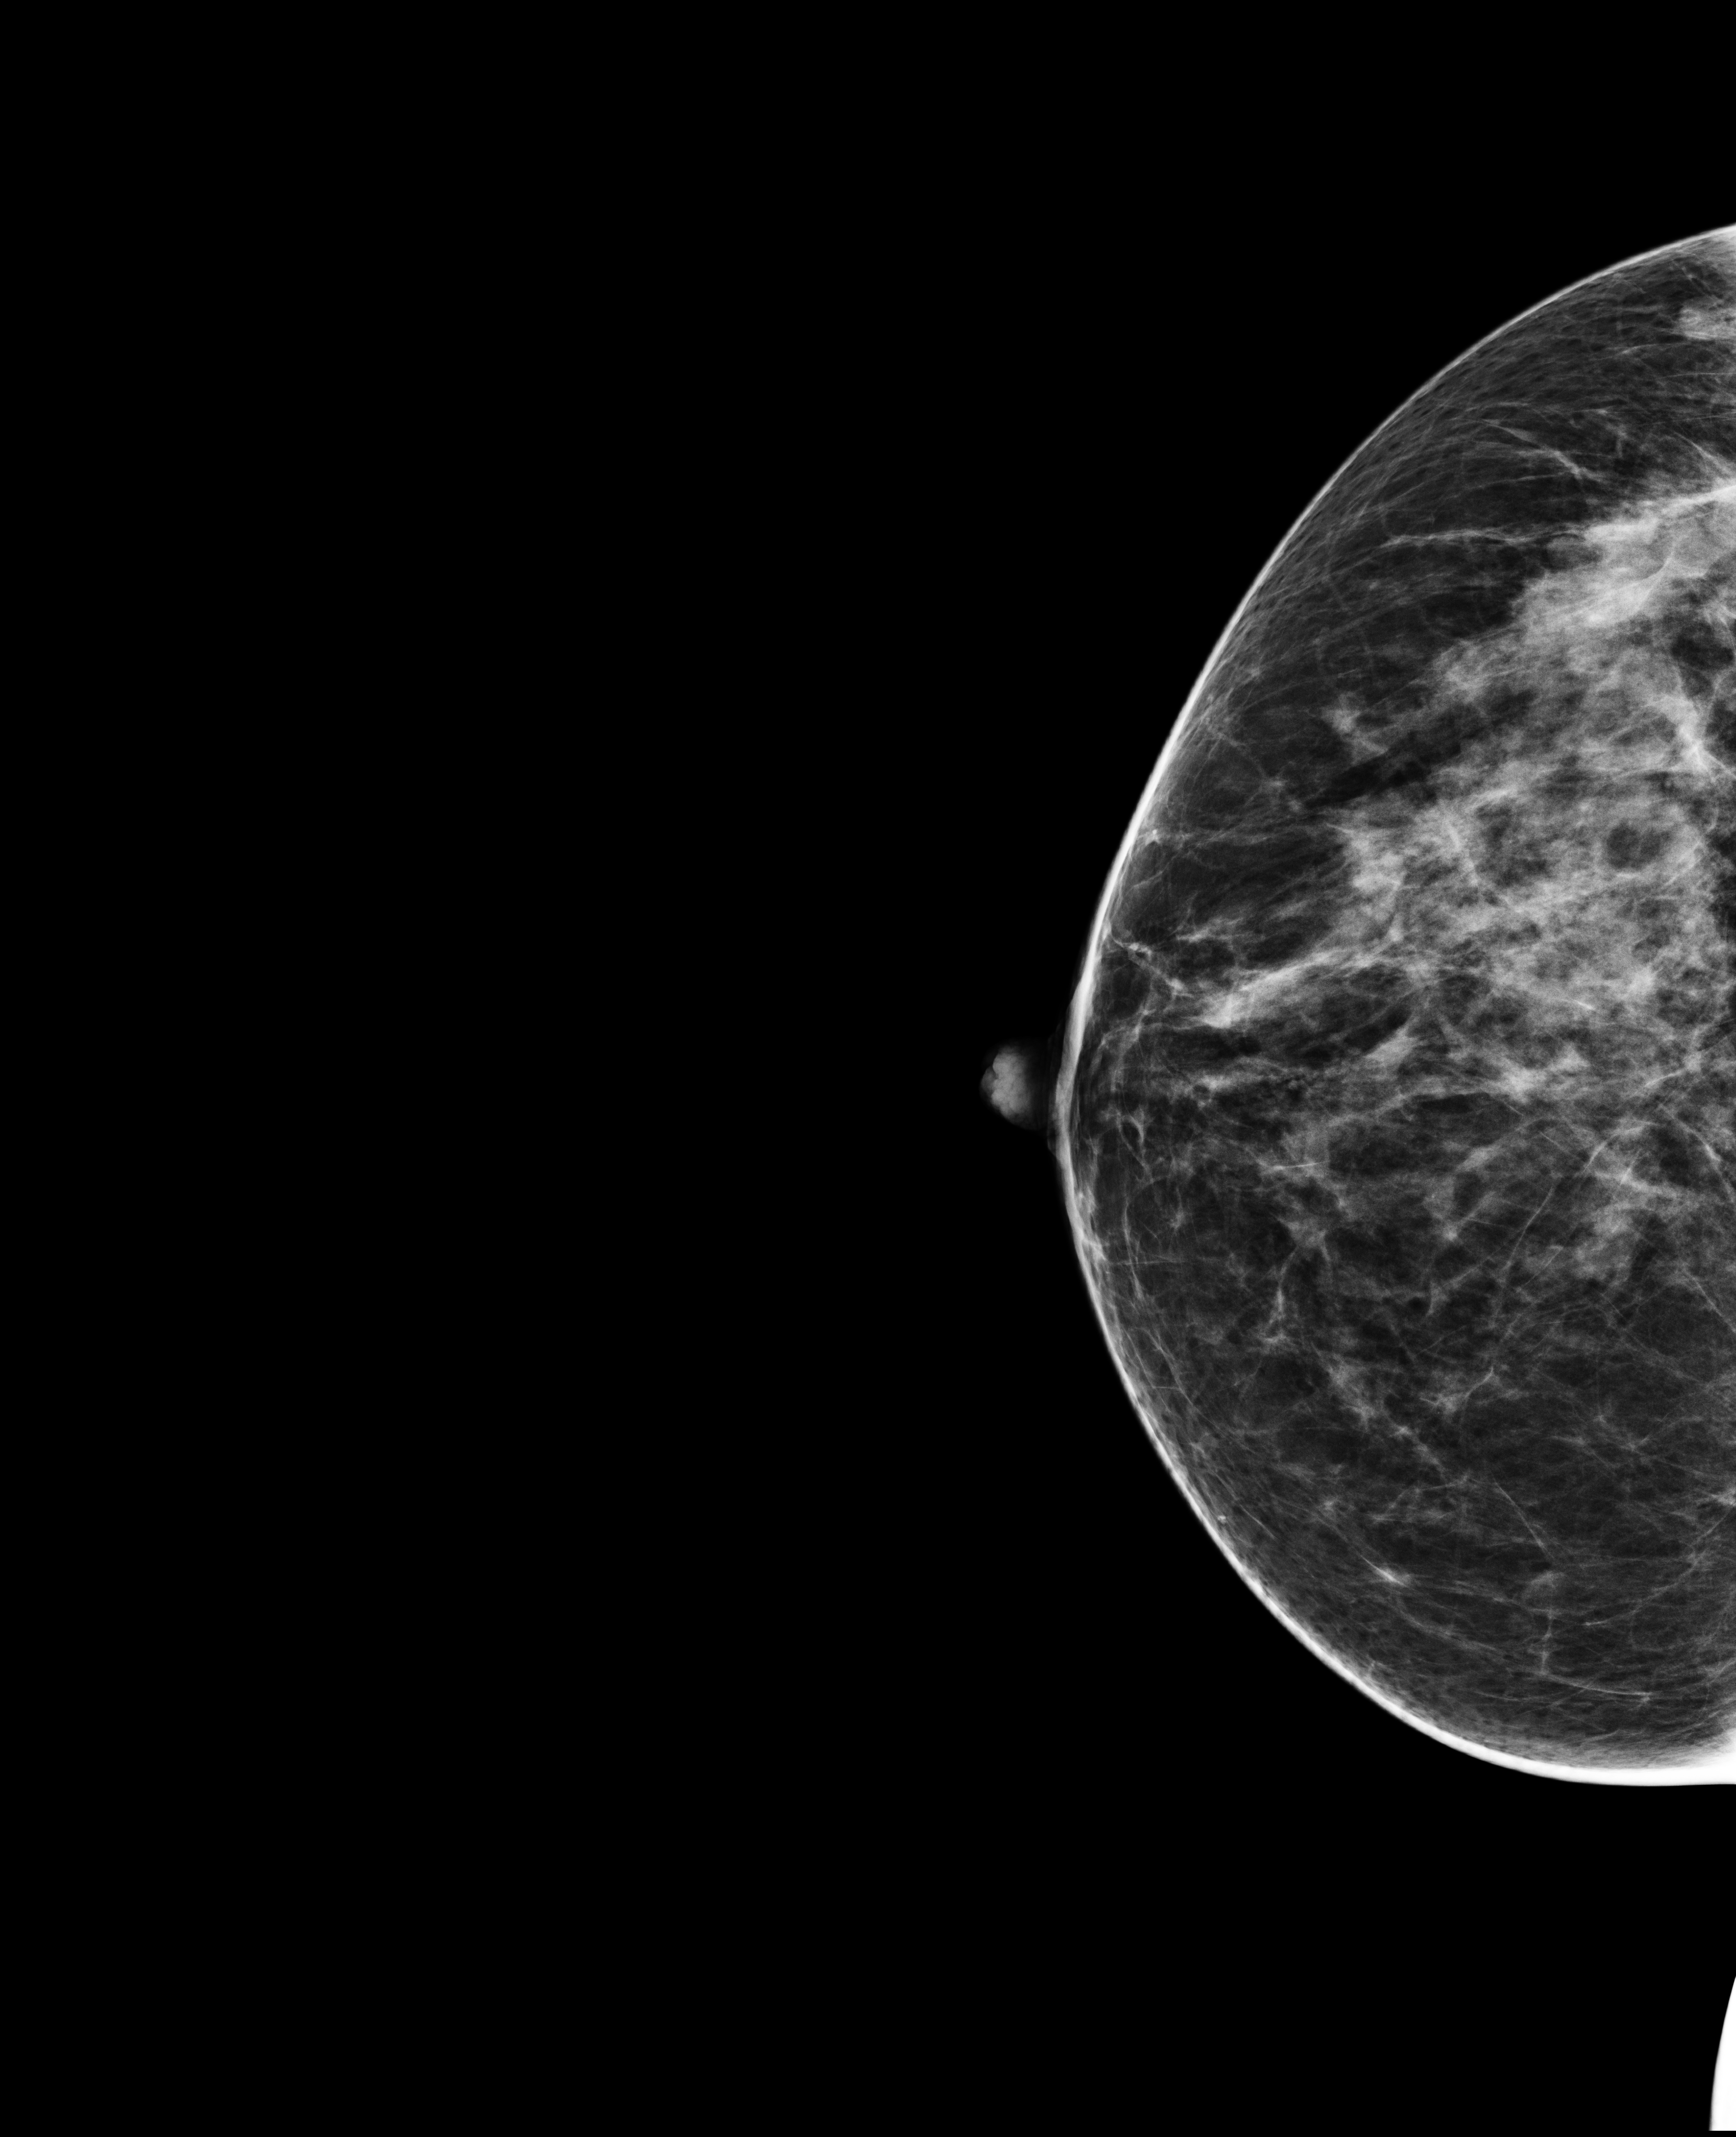
Annual screening mammography examination, system: Selenia Dimensions.
Image type: full-field digital mammogram. Breast: right. Projection: cranio-caudal projection.